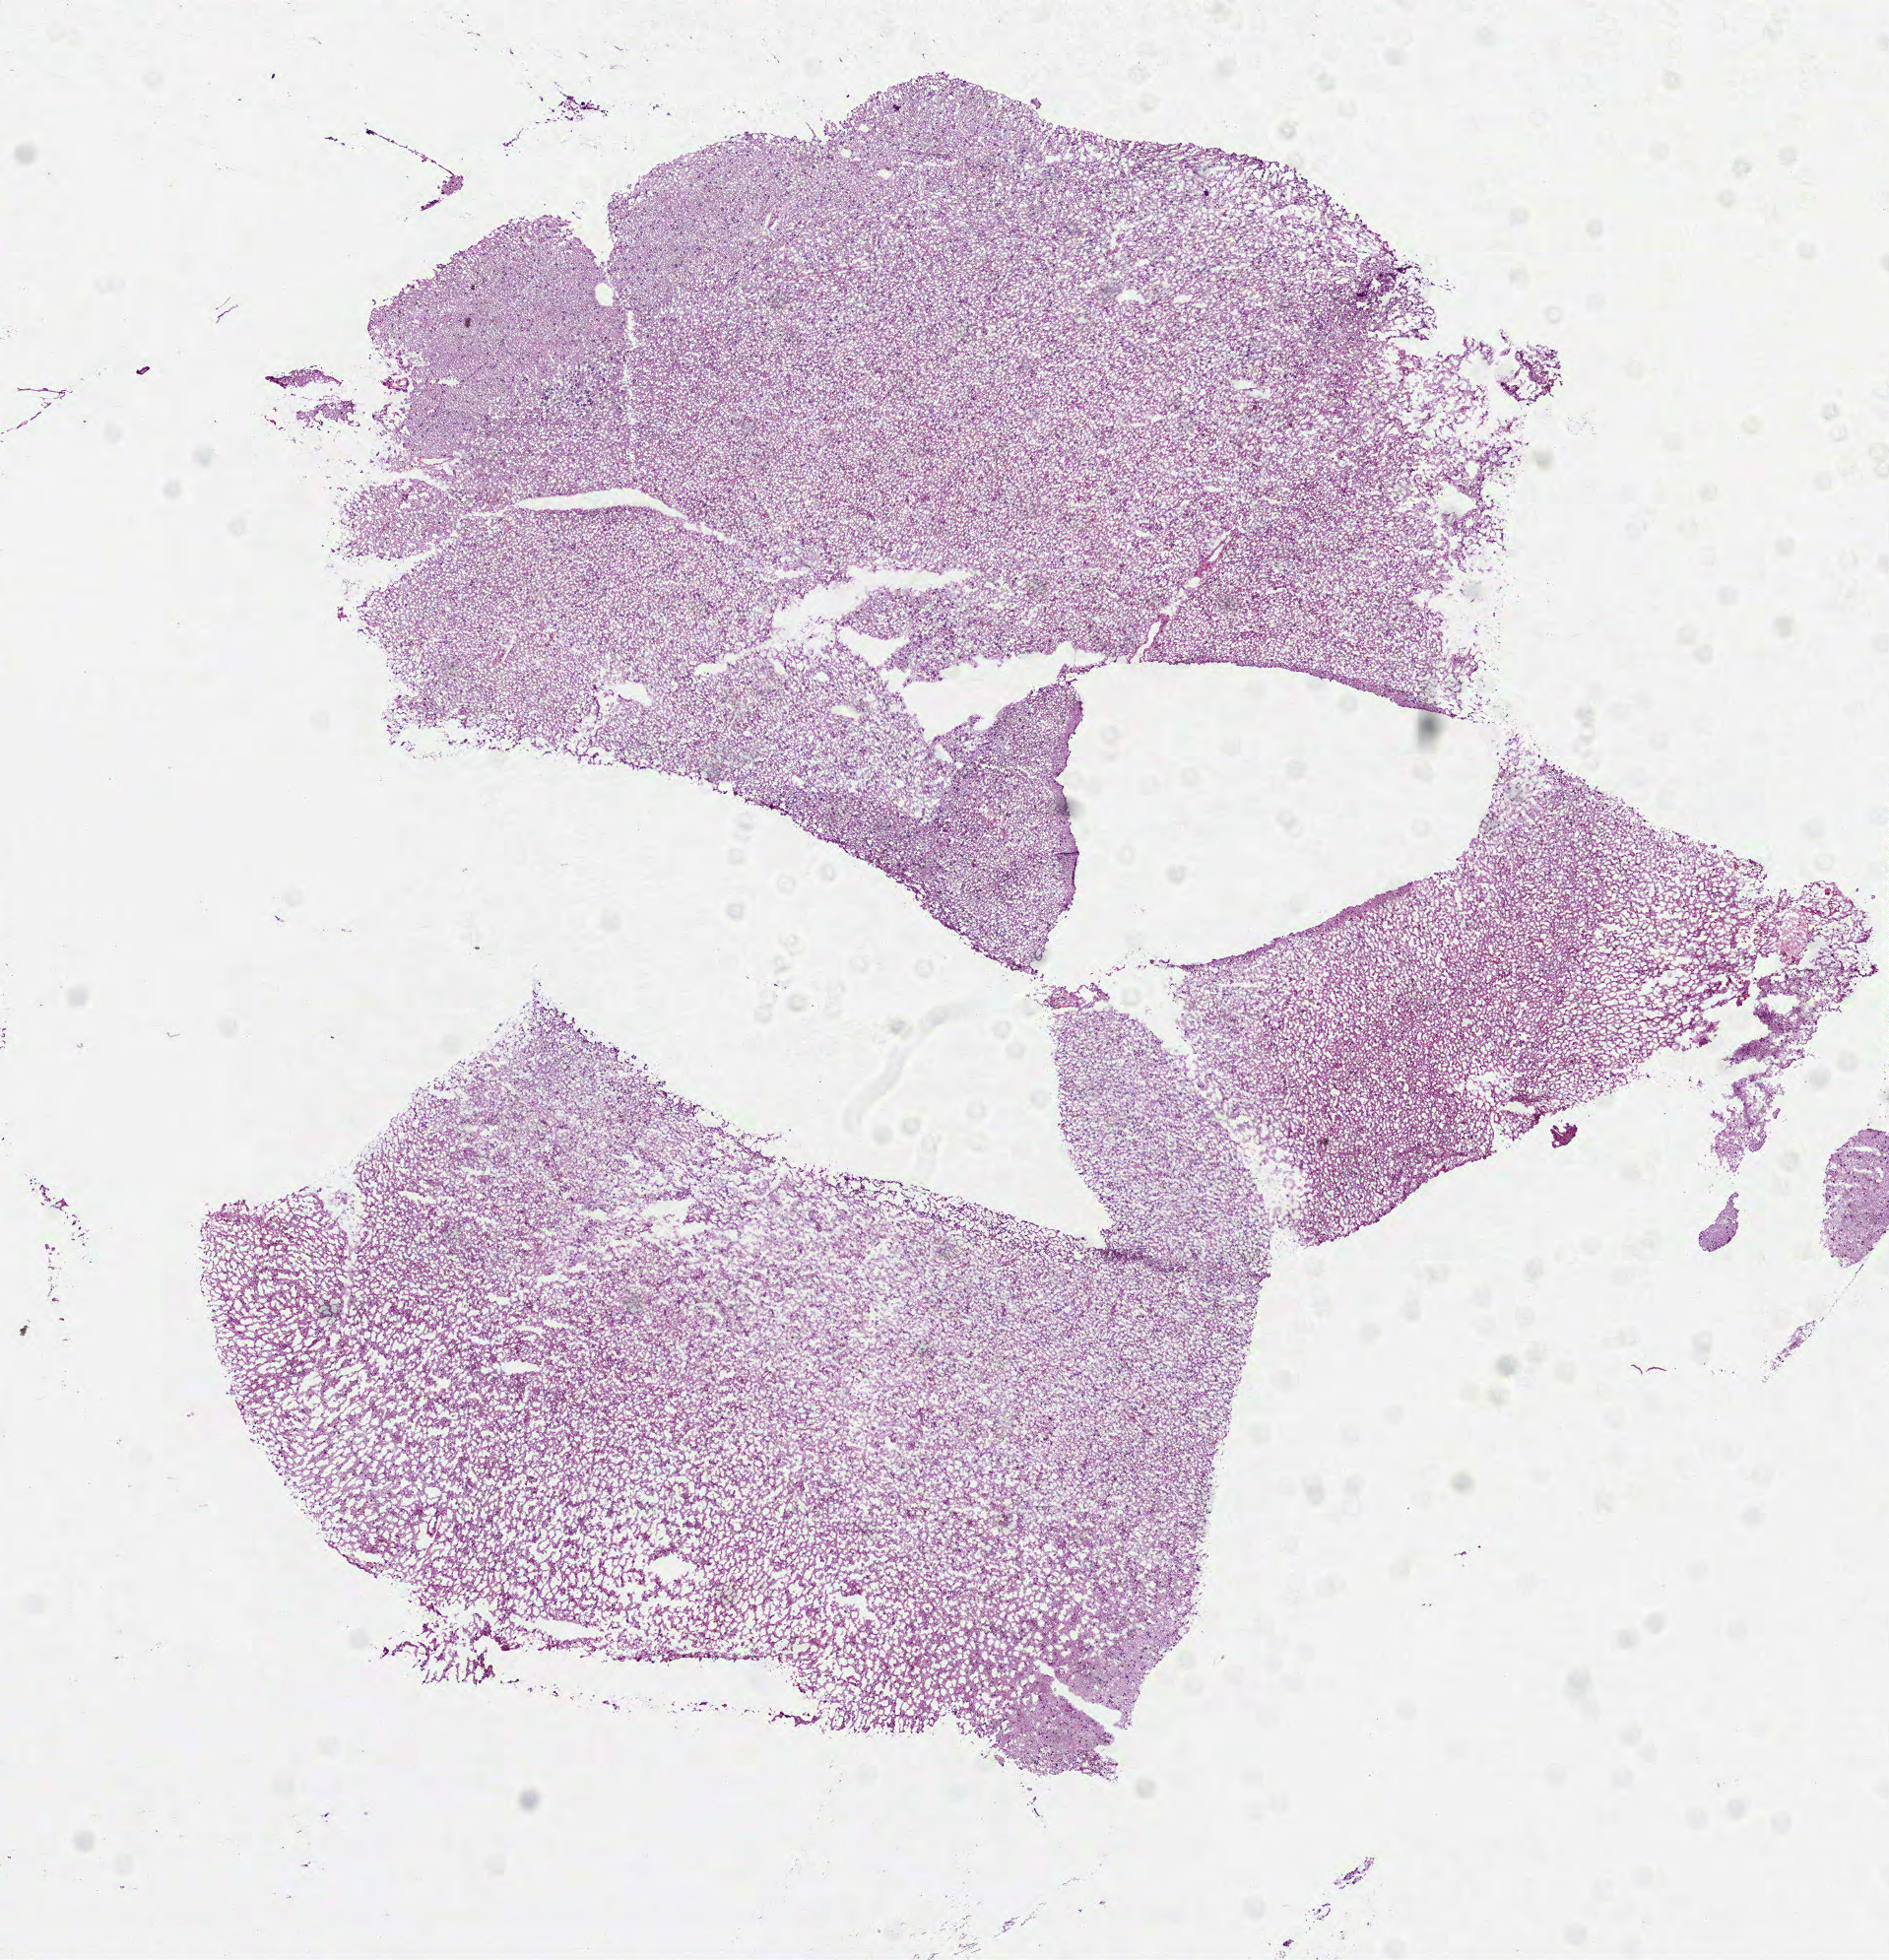
Whole-slide histology image, Hematoxylin and eosin (H&E) stained, shown as a low-resolution overview of the whole scanned area (about 7.7 x 8.0 mm), frozen section from the bottom of the tissue portion, primary tumour sample from the brain. Male, age 33 years at initial diagnosis. Slide review estimates, as recorded: tumour cells 100%, tumour nuclei 55%.
Pathologic diagnosis: Oligodendroglioma, NOS.